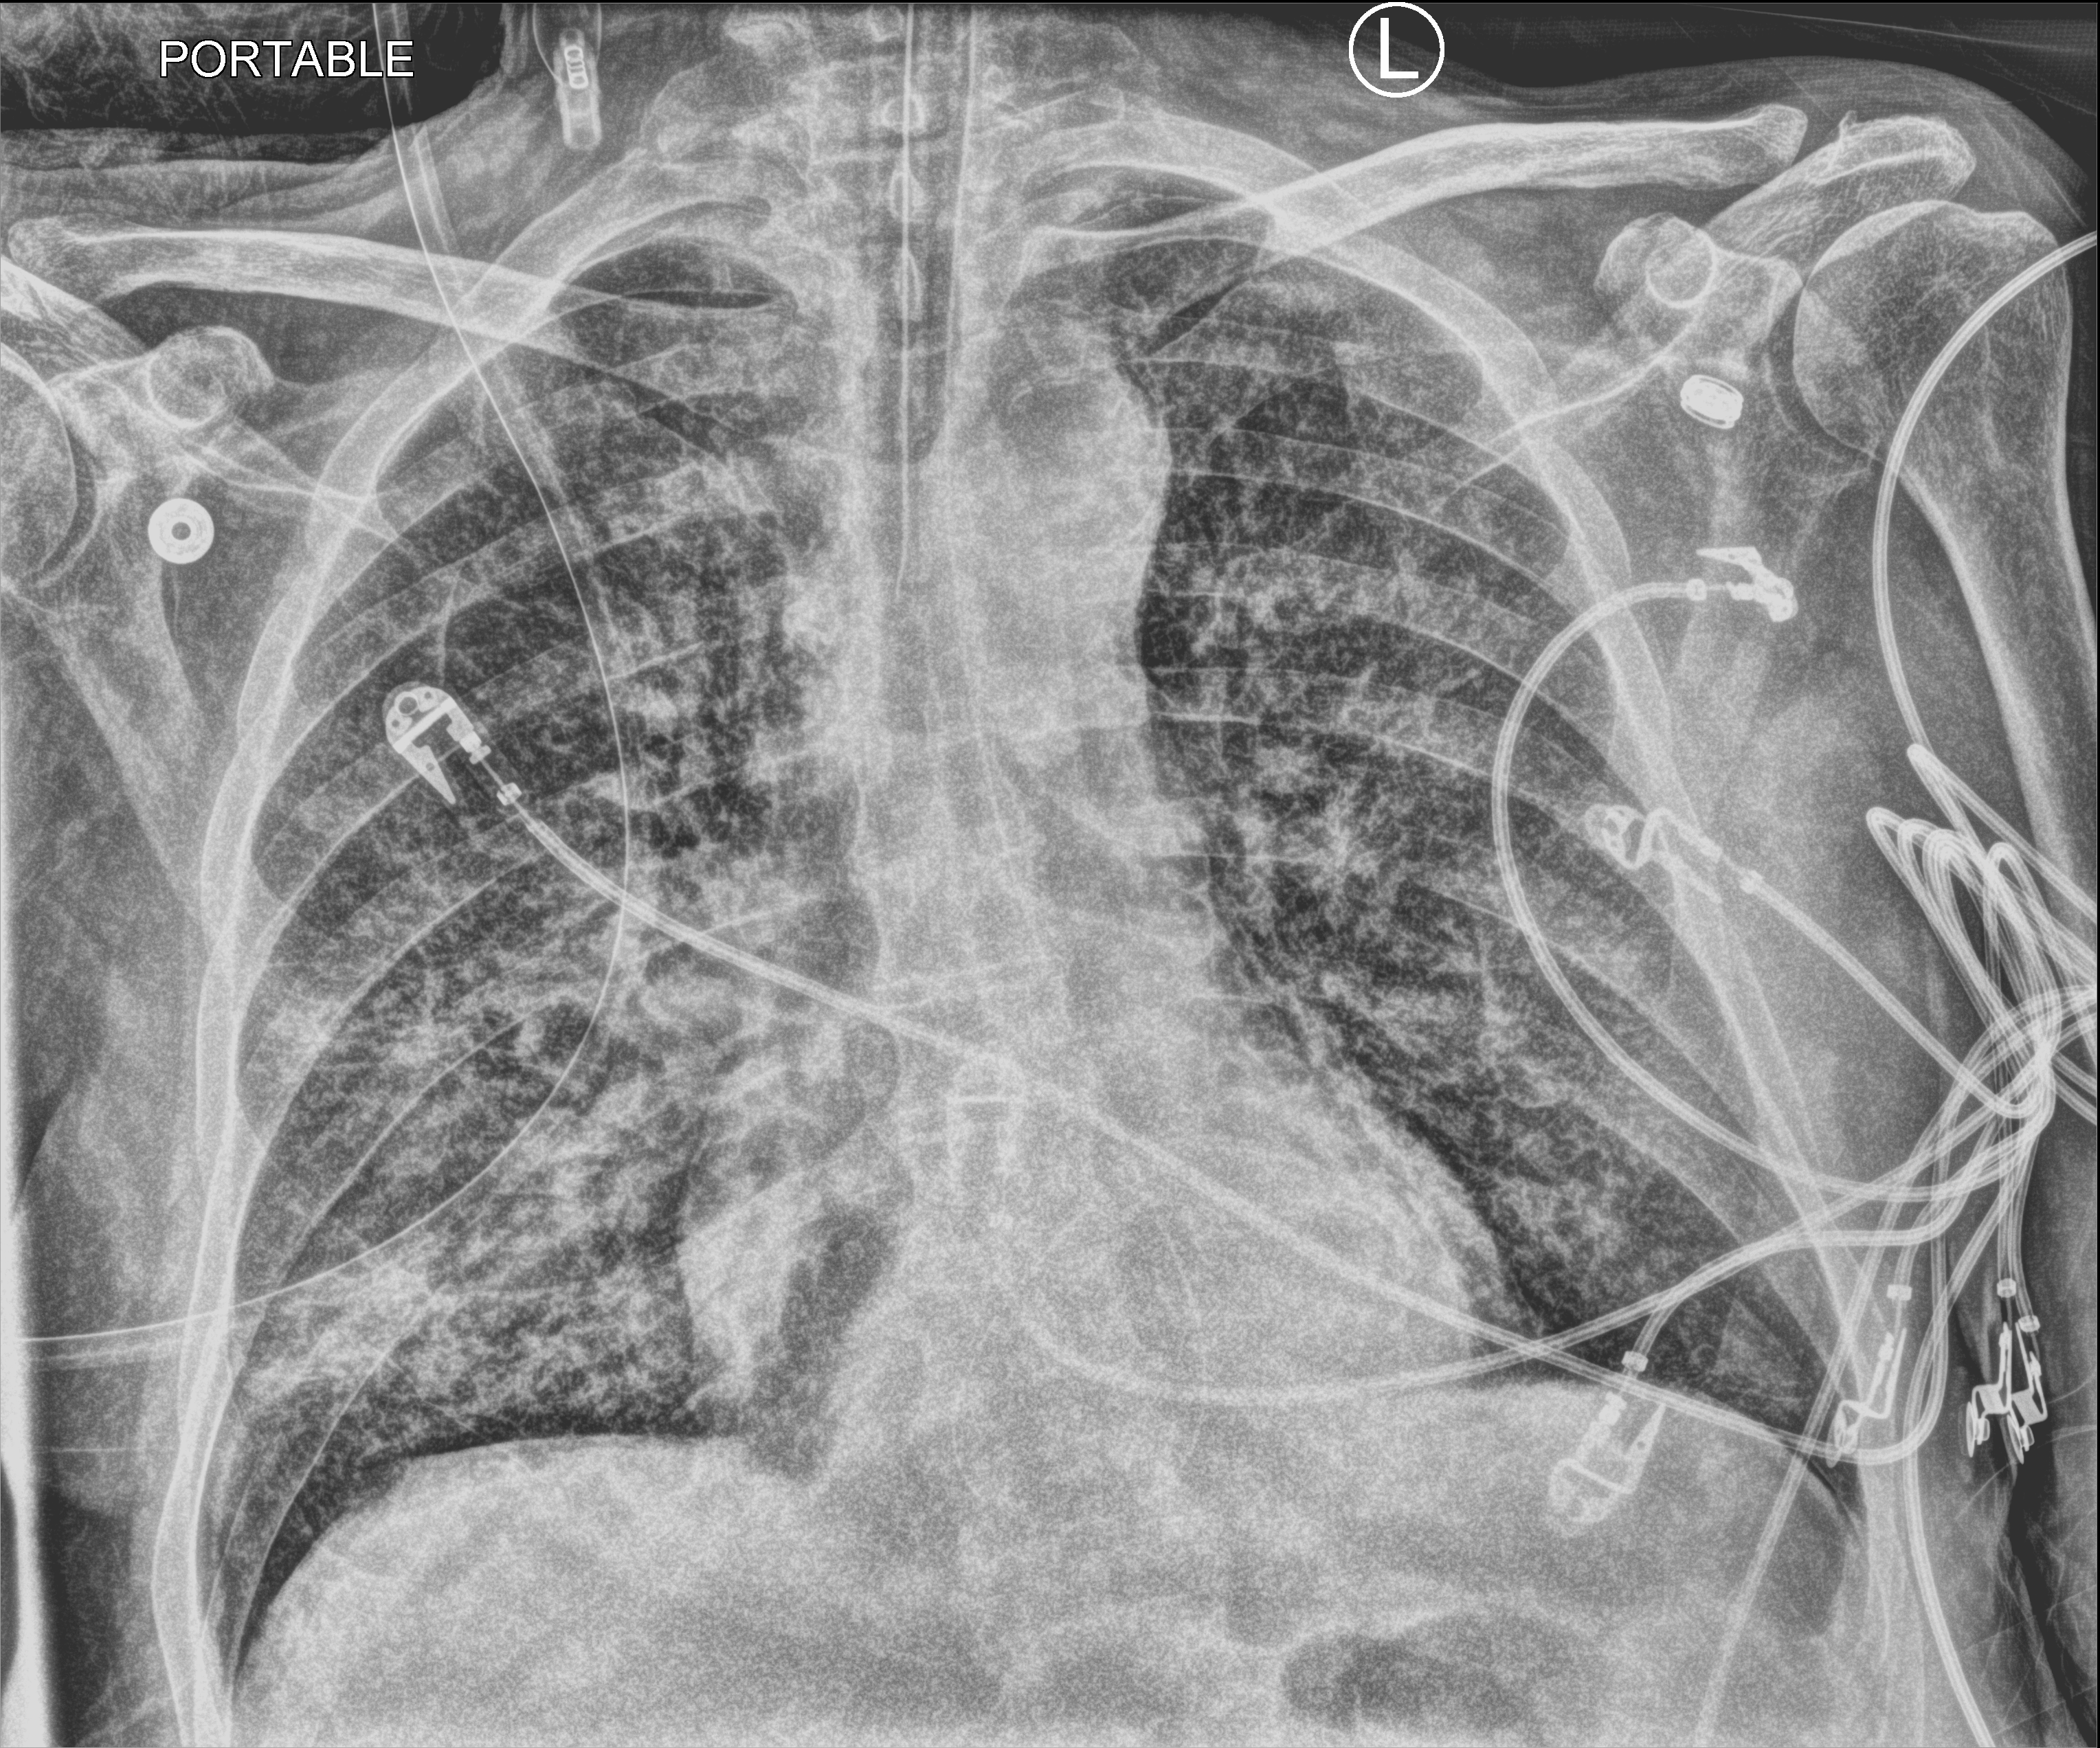
Bedside chest radiograph (computed radiography); anteroposterior (AP) projection. Male patient hospitalised with COVID-19, age 75–90 years.
From the hospital-stay record, not from the radiograph (when in the stay this image was taken is not recorded): admitted to intensive care during this hospital stay: yes; mechanically ventilated during this hospital stay: yes; length of hospital stay: 10 days.